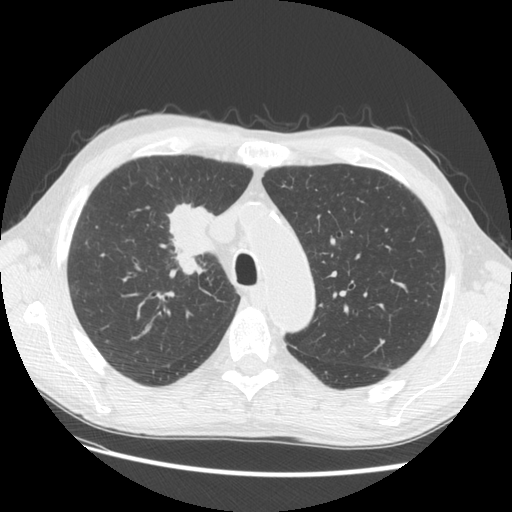
Axial slice from a low-dose chest CT screening exam, third screening round (two years after baseline), lung window (W 1500 / L -600 HU), standard (soft-tissue) reconstruction kernel (STANDARD), slice 35 of 133 in the series. Male participant, aged 73 years at enrolment. Current smoker at enrolment.
• Expert-annotated lung lesion, bounding box (x1, y1, x2, y2) in pixels: (142, 183, 233, 279).
• The screening reader recorded 4 non-calcified nodules or masses ≥4 mm on this exam; which of them this box marks is not recorded.
• Official screen result: positive, other.
• Participant outcome: lung cancer diagnosed 48 days after this screen — squamous cell carcinoma, NOS, right upper lobe, poorly differentiated (G3), stage IIIB (AJCC 6th edition), 56 mm at pathology.